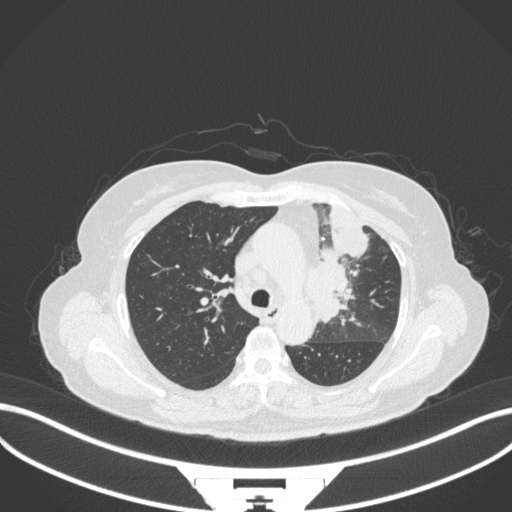
Chest CT, one axial slice. Position 231 of 382 along the scan axis. Lung window (W 1500 / L -600 HU). 512 × 512 image matrix, field of view 400 × 400 mm. Female patient, age 64 years. From the clinical record (not read from this slice): clinical TNM (as recorded): T2a N2 M0.
Annotated regions visible in this slice (rectangle marked by the reading radiologist):
- lung tumour (recorded histology: adenocarcinoma): bounding box (x1, y1, x2, y2) in pixels: (306, 243, 354, 328)
- lung tumour (recorded histology: adenocarcinoma): (329, 203, 373, 258)